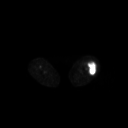
FDG PET of an extremity soft-tissue mass (from a PET/CT study), one axial slice; position 204 of 267 along the scan axis; 128 × 128 image matrix, field of view 700 × 700 mm. Female patient, age 62 years. From the clinical record (not read from this slice): histological type: undifferentiated – high grade; grade: high; site of the primary tumour: left thigh.
Structures marked on this image (expert contour drawn on MRI and transferred to this co-registered scan by the dataset authors):
- gross tumour volume including surrounding oedema: box from (x=84, y=60) to (x=96, y=75) px
- gross tumour volume (mass): (x=89, y=62)–(x=96, y=75)